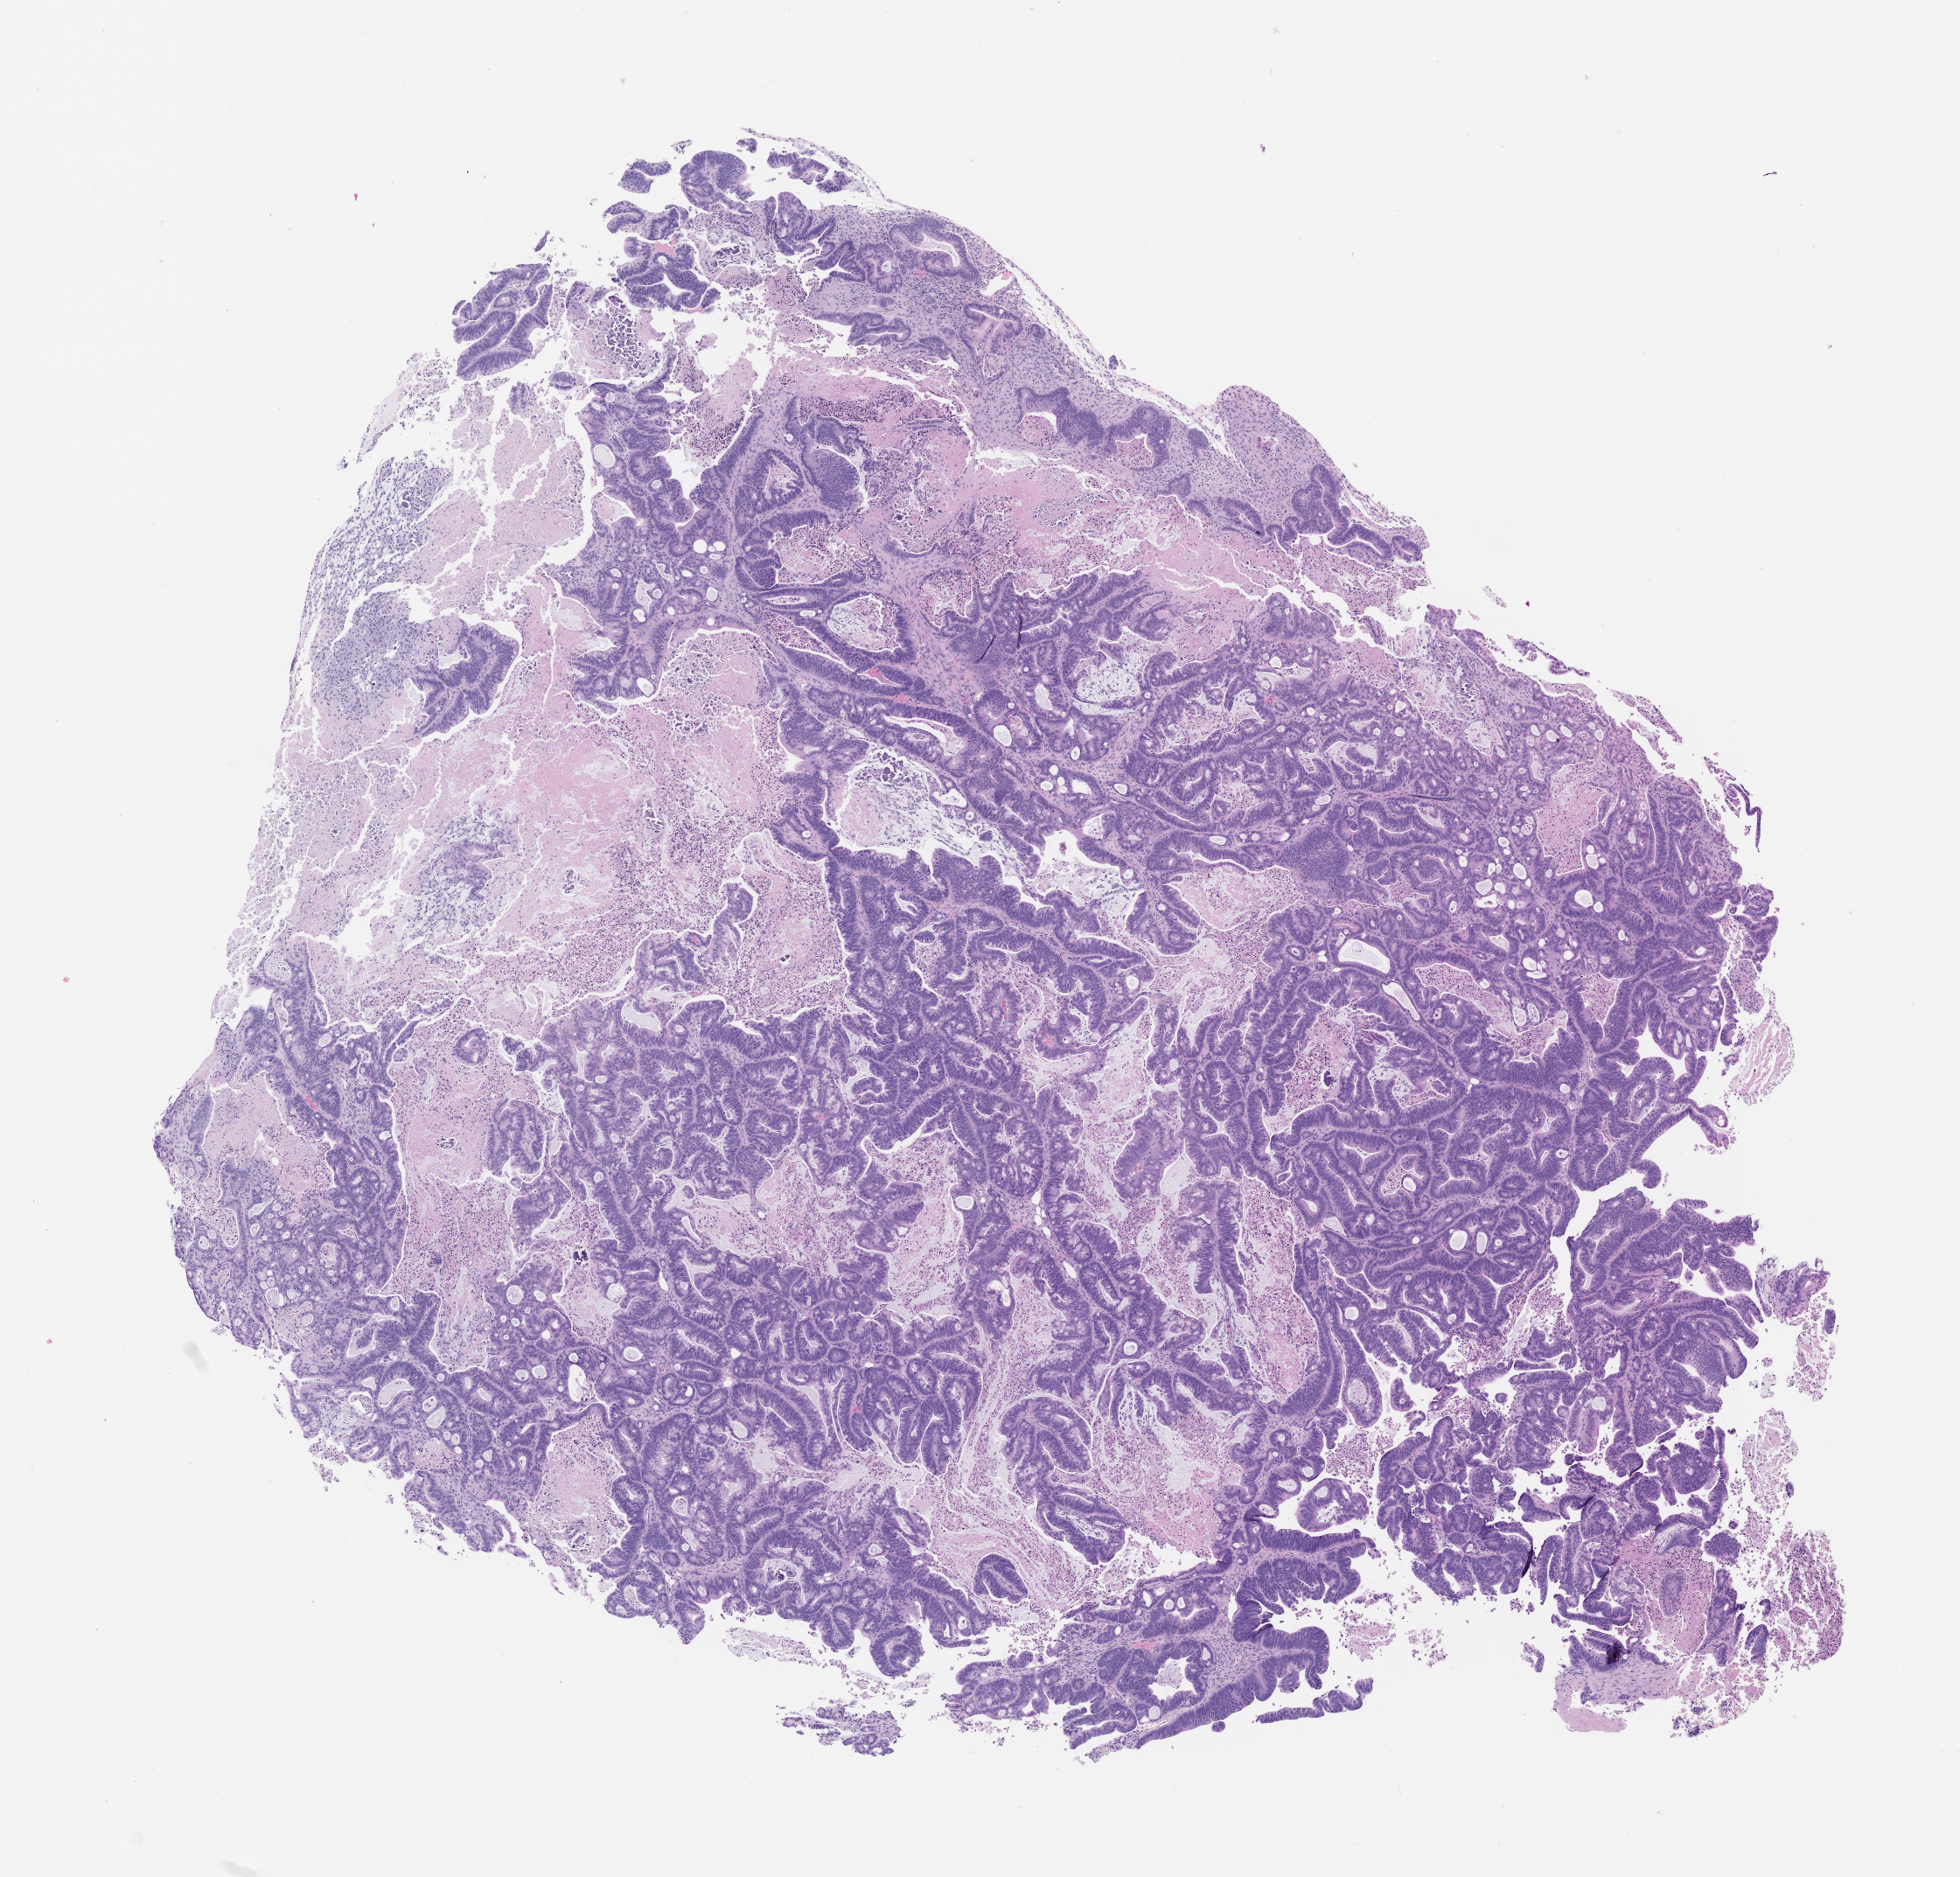
Hematoxylin and eosin (H&E) whole-slide image of a patient-derived xenograft (PDX) tumor grown in a mouse, passage 2 — low-resolution overview of the scanned area, about 9.0 x 8.6 mm, formalin-fixed, paraffin-embedded (FFPE) tissue, tumor site category: colon.
• originating patient diagnosis: Colon Adenocarcinoma